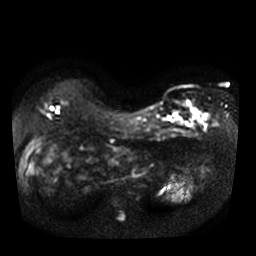
Breast MRI, one axial slice. Slice 17 of 36 in the series (ordered by position). Diffusion-weighted series; image 2 of 4 stored at this slice position (different b-values; order by instance number). 3 T. 256 × 256 image matrix, field of view 320 × 320 mm. Female patient.
Structures marked on this image (manually delineated by an expert):
- tumour on diffusion-weighted imaging: bounding box <187,101,206,119> (left, top, right, bottom; pixels)